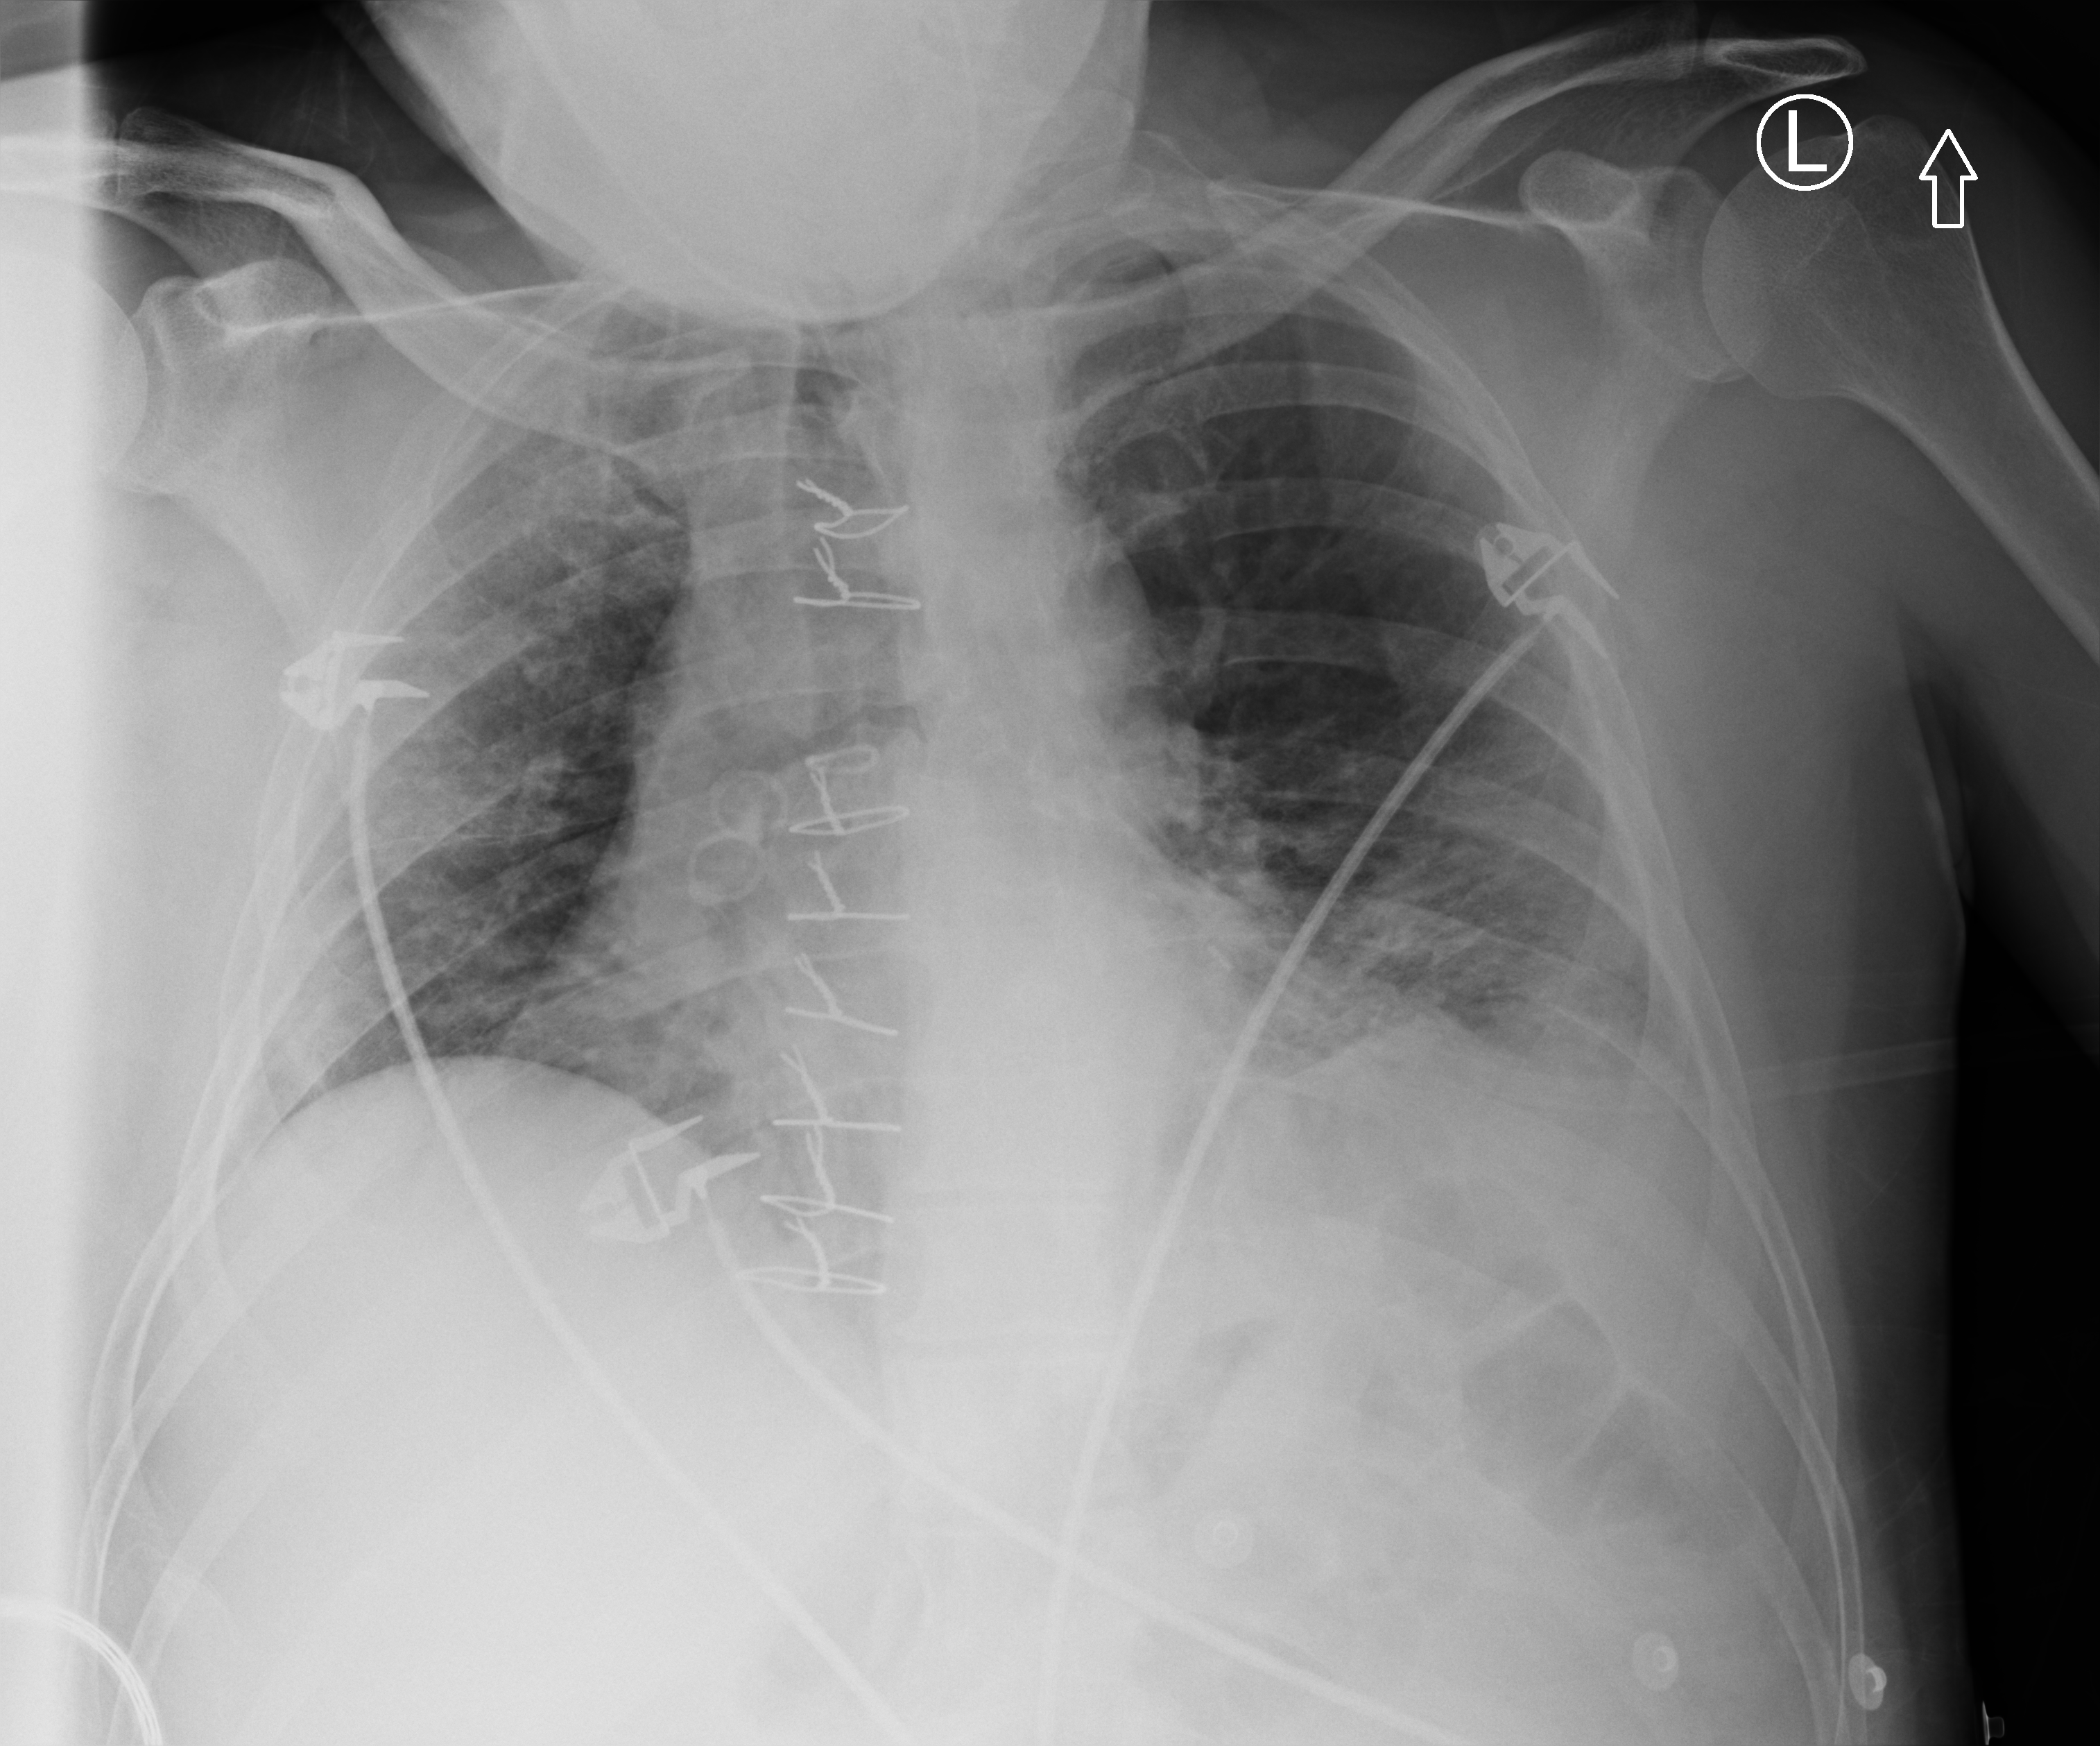
Chest X-ray (portable); anteroposterior (AP) projection. Patient hospitalised with COVID-19; male, aged 18–59 years.
Hospital-stay facts (about this admission, not read from this image; timing relative to this image not recorded): smoking status (admission record): former; length of hospital stay: 63 days.